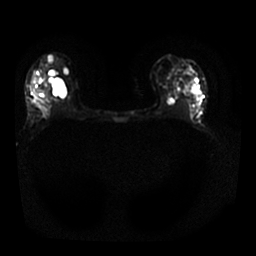
Breast MRI, one axial slice; position 13 of 25 along the scan axis; diffusion-weighted series; image 2 of 4 stored at this slice position (different b-values; order by instance number); 1.5 T; 4 mm slice thickness; 256 × 256 image matrix, field of view 330 × 330 mm. Female patient.
Outlined on this slice (outlined manually by an expert reader):
- tumour on diffusion-weighted imaging: box from (x=33, y=99) to (x=51, y=122) px